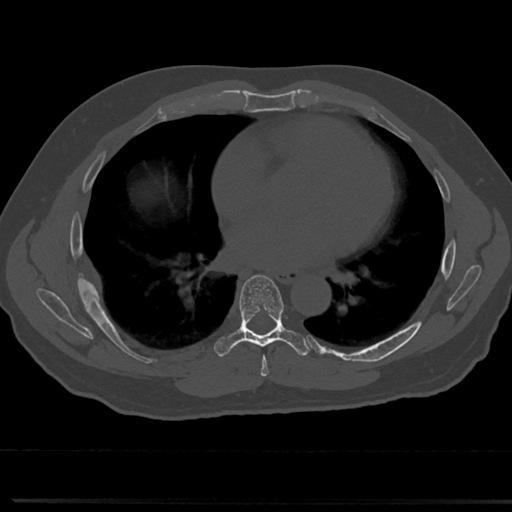
CT including the spine, one axial slice. Position 411 of 817 along the scan axis. Reconstruction kernel Br40s/3. 120 kVp. Bone window (W 1800 / L 400 HU). 512 × 512 image matrix. Male patient, age 61 years. From the clinical record (not read from this slice): primary cancer: prostate.
Structures marked on this image (semi-automatically segmented with operator editing):
- T6 vertebra: bounding box [x1, y1, x2, y2] px = [252, 336, 319, 367]
- T7 vertebra: [217, 274, 305, 356]